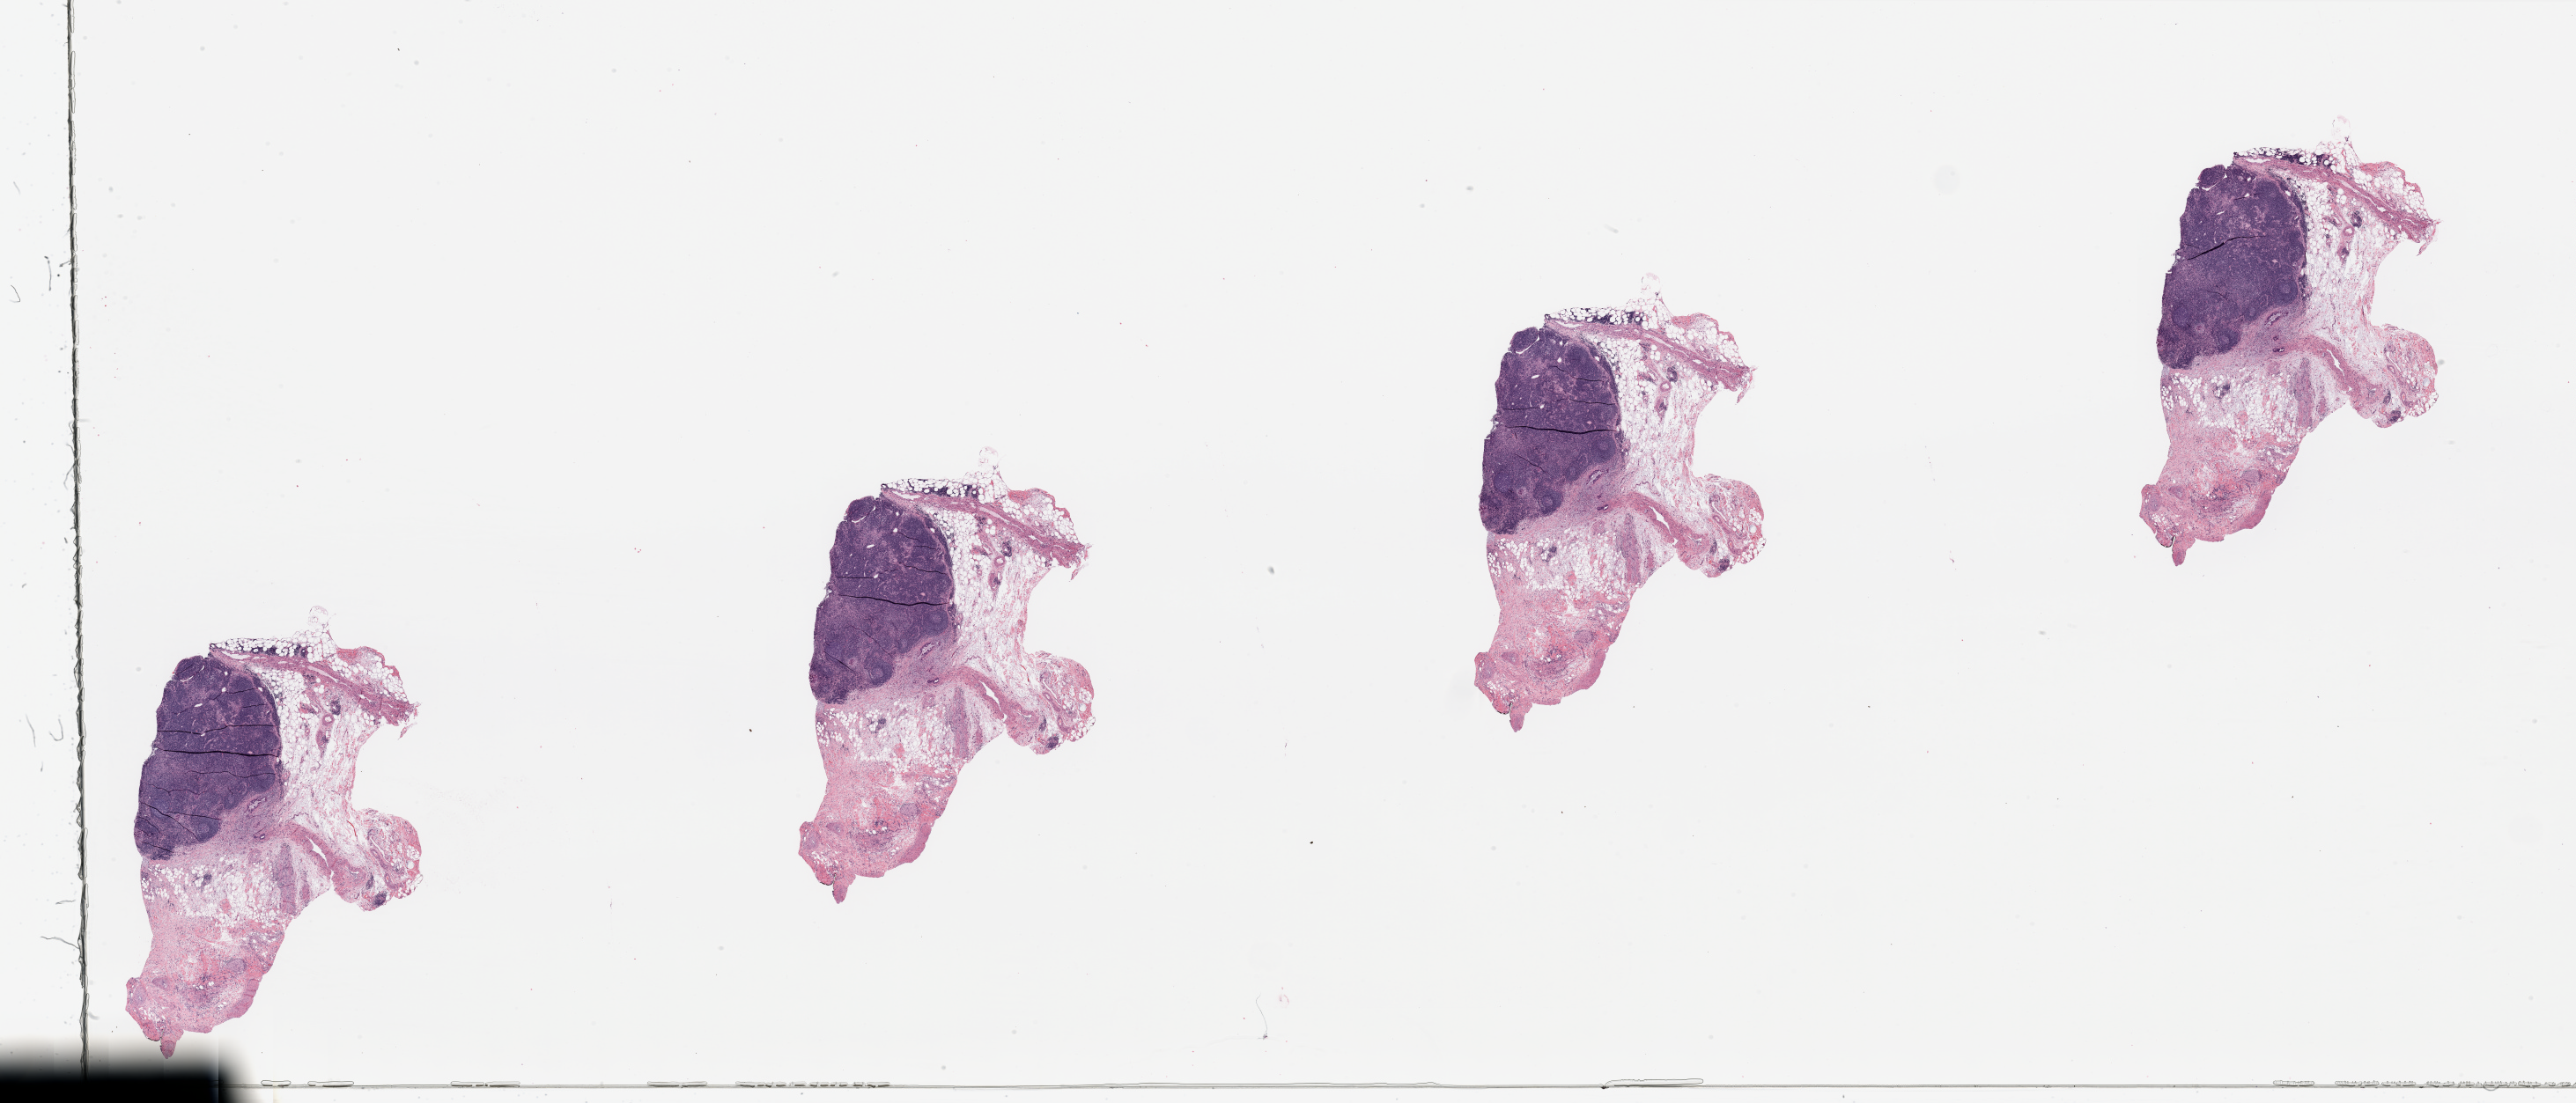
Whole-slide histology image, H&E — low-resolution overview of the scanned area, about 46.3 x 19.8 mm (acquisition: 20x scan). Tumour tissue sample, pancreas. Patient: female, age 74 years.
Primary tumour site (as recorded): head. Patient diagnosis (cohort enrolment): ductal adenocarcinoma (pancreas).